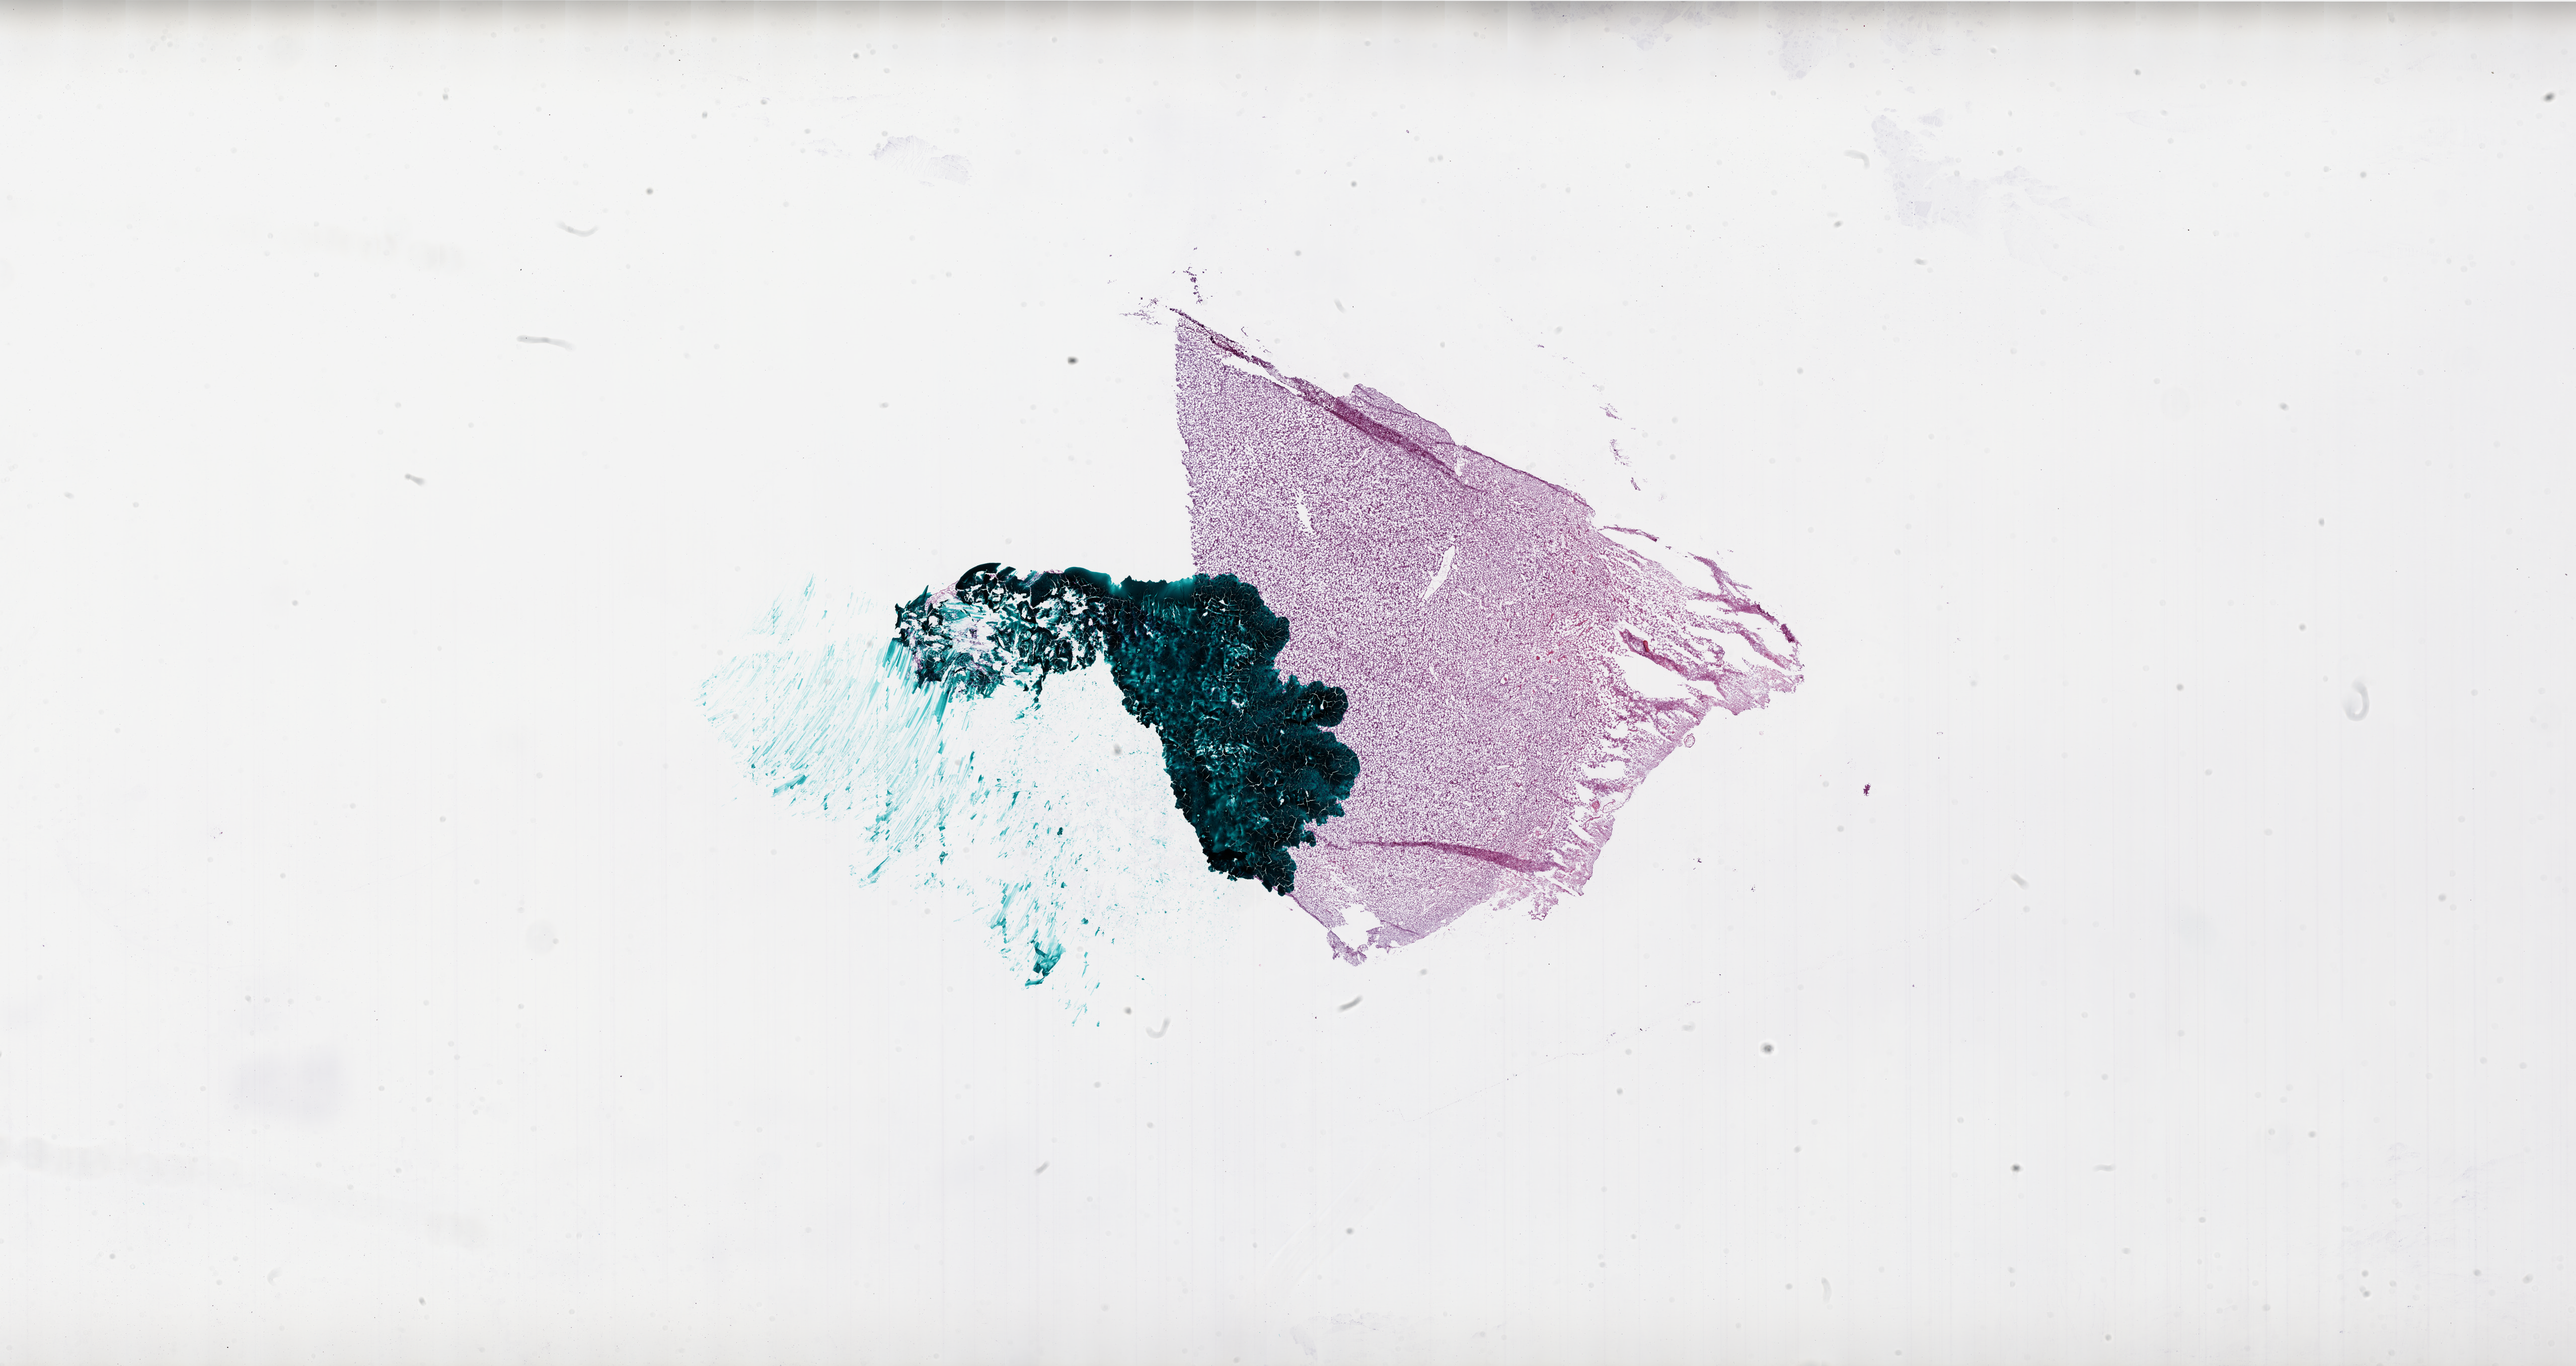
Whole-slide histology image, H&E-stained, whole scanned area (about 41.0 x 21.7 mm, acquisition: 20x scan) shown as a low-resolution overview. Frozen section from the bottom of the tissue portion. Primary tumour sample from the brain. Male patient; age at initial diagnosis 54 years. Pathologist review of this section (percent, as recorded): tumour cells 75%, tumour nuclei 80%, normal cells 0%, stromal cells 0%, necrosis 25%.
Pathologic diagnosis: Glioblastoma.